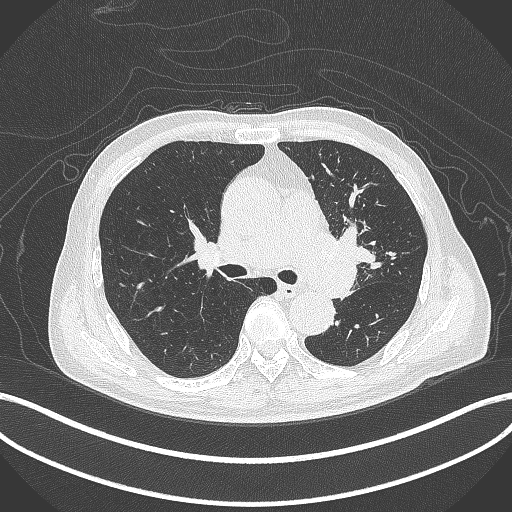
Chest CT, one axial slice. Slice 264 of 417 in the series (ordered by position). 120 kVp. Lung window (W 1500 / L -600 HU). 512 × 512 image matrix, field of view 400 × 400 mm. Male patient, age 77 years. From the clinical record (not read from this slice): clinical TNM (as recorded): T3 N1 M0.
Outlined on this slice (bounding box drawn by a radiologist):
- lung tumour (recorded histology: adenocarcinoma): bounding box <306,228,369,301> (left, top, right, bottom; pixels)